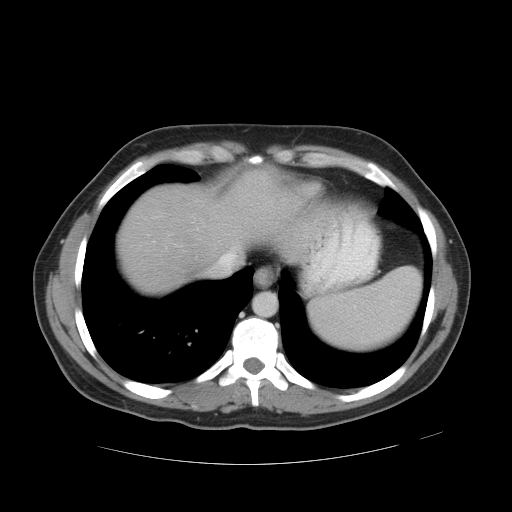
Contrast-enhanced abdominal CT, one axial slice; slice 44 of 49 in the series (ordered by position); reconstruction kernel STANDARD; 120 kVp; intravenous contrast given; soft-tissue window (W 400 / L 40 HU); 5 mm slice thickness; 512 × 512 image matrix, field of view 422 × 422 mm. Male patient, age 42 years. From the clinical record (not read from this slice): diagnosis: colorectal cancer liver metastases, imaged before liver resection; multiple liver metastases: yes; largest metastasis: 2.8 cm.
Outlined on this slice (expert manual segmentation):
- hepatic veins: bounding box (x1, y1, x2, y2) in pixels: (196, 227, 237, 274)
- liver: (119, 169, 303, 294)
- planned liver remnant (the part of the liver to remain after resection): (120, 169, 304, 294)